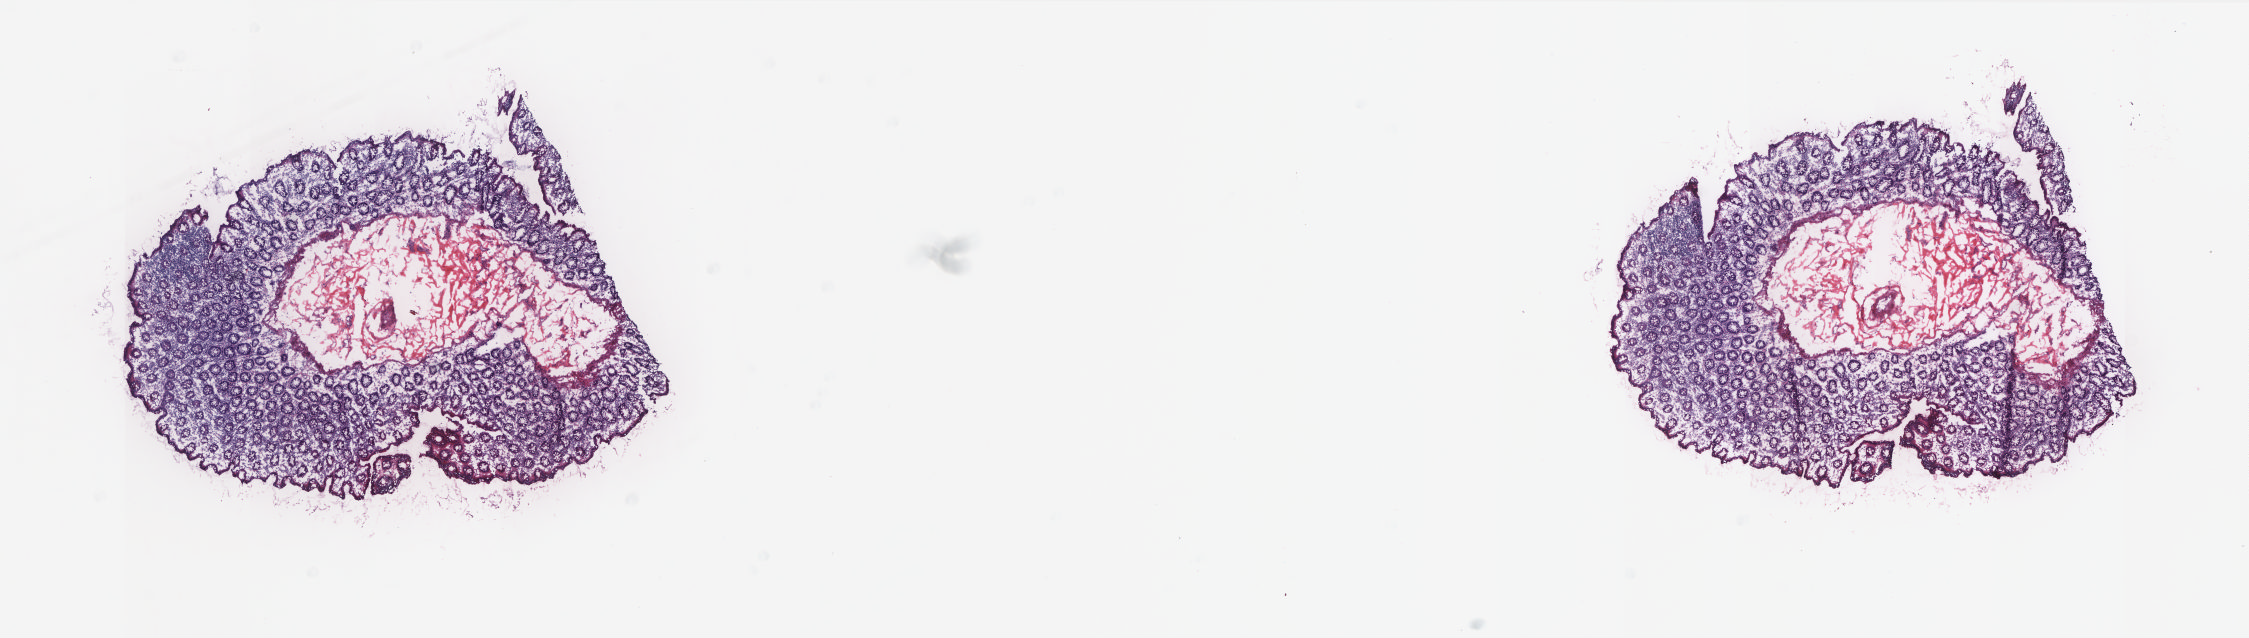
Whole-slide histology image, H&E-stained — a low-resolution overview of the entire scanned area, about 18.0 x 5.1 mm (from a 20x scan), frozen section from the top of the tissue portion, sample: solid tissue normal (non-tumour tissue), colon. Female, age 88 years at initial diagnosis. Slide review estimates, as recorded: tumour cells 0%, normal cells 100%. Infiltration values recorded for this section: lymphocyte infiltration 35%, monocyte infiltration 10%, neutrophil infiltration 0%.
- this section: solid tissue normal sample (biorepository sample class)
- patient diagnosis: Adenocarcinoma, NOS